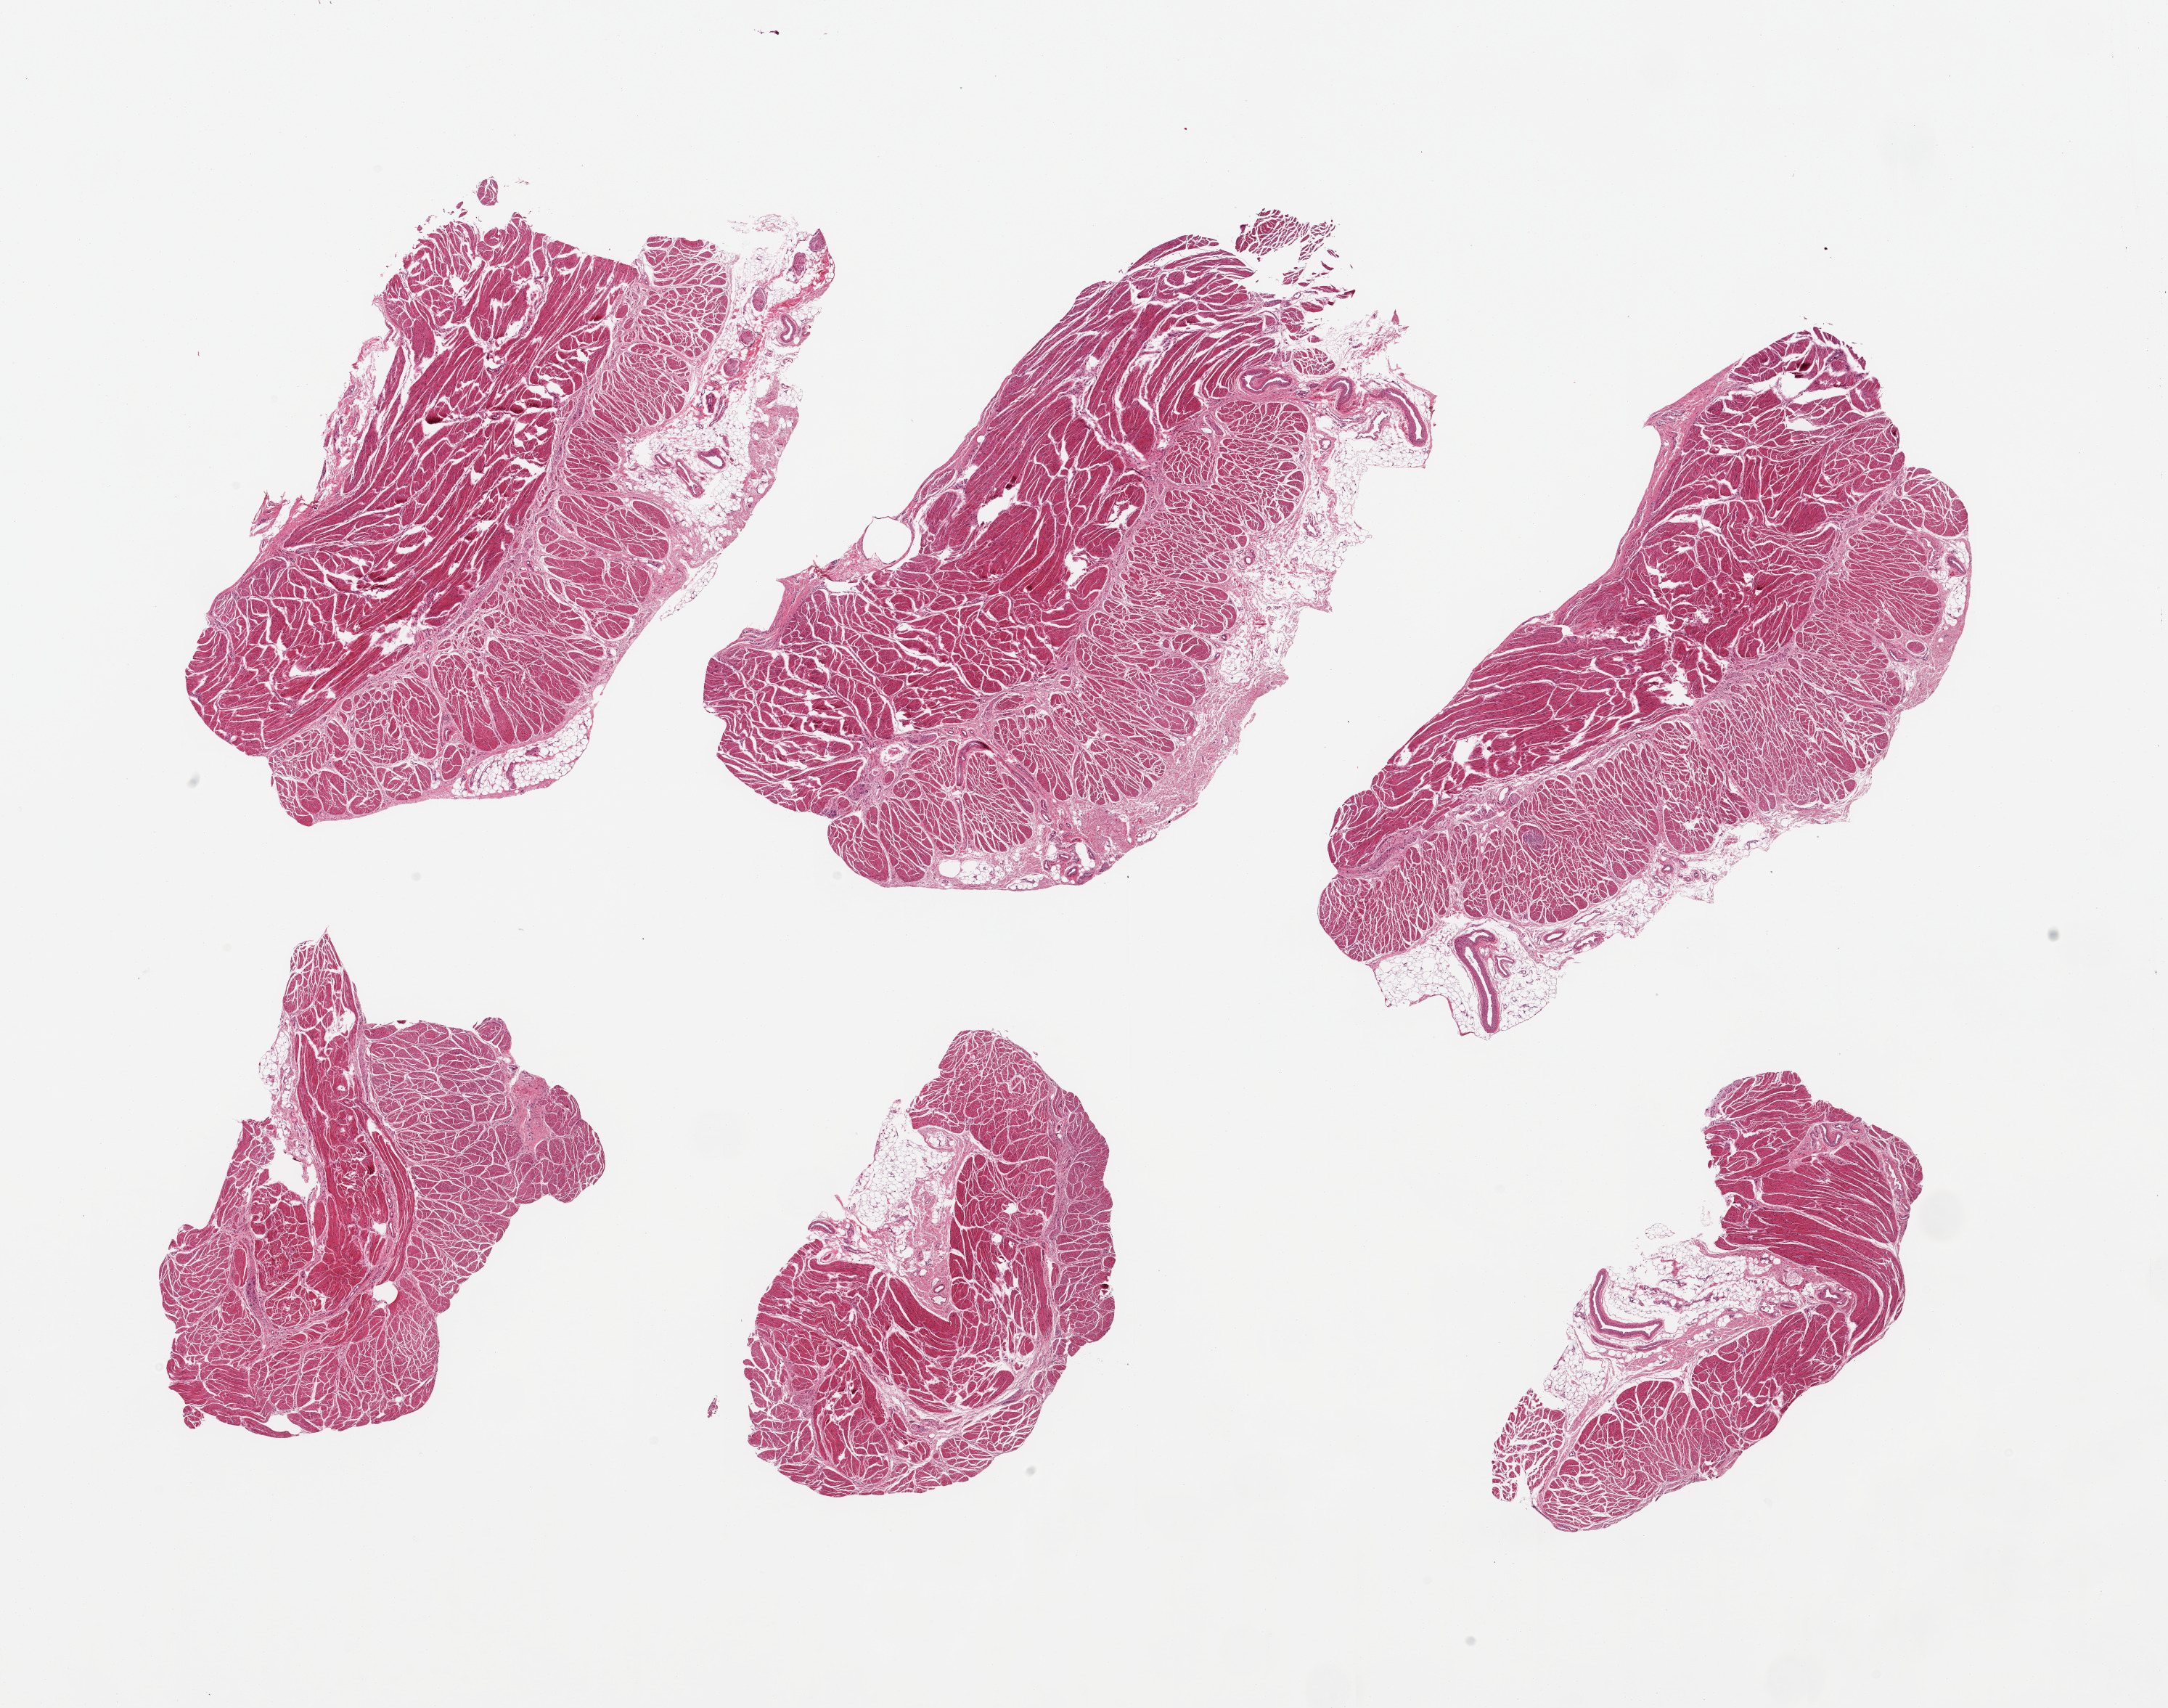
Digitized H&E-stained section, brightfield, shown as a low-resolution overview of the whole scanned area (about 23.6 x 18.6 mm, slide scanned at 20x); PAXgene-fixed, paraffin-embedded tissue; sampled site (target tissue): esophageal muscle; tissue donor sample. Donor: male.
Pathologist's review note for this sample: 6 pieces, confirmed target muscularis, adherent fibroadipose nubbins.